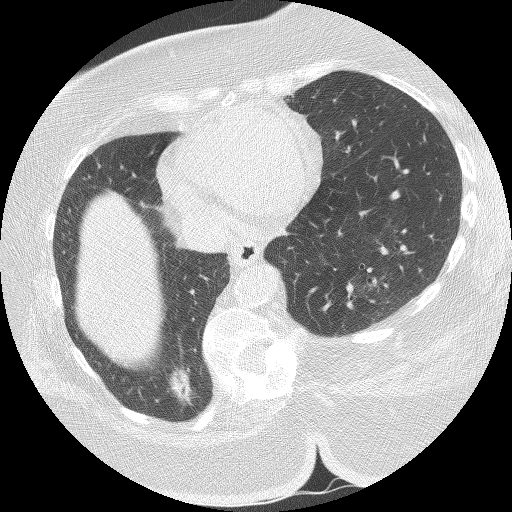
Chest CT (low-dose screening protocol), one axial image; first (baseline) screen; lung window (W 1500 / L -600 HU); 2.5 mm slice thickness; lung (sharp) reconstruction kernel (BONE); 512 × 512 image matrix, field of view 340 × 340 mm. Female participant, aged 59 years at enrolment. Former smoker at enrolment.
- Expert-annotated lung lesion, bounding box <144,347,204,417> (left, top, right, bottom; pixels).
- The exam's reader record, not a measurement of the box and not confirmed to be the same lesion: non-calcified nodule or mass ≥4 mm, right lower lobe, 21 × 10 mm, spiculated (stellate) margins, soft tissue attenuation.
- Official screen result: positive, change unspecified: nodule(s) >= 4 mm or enlarging nodule(s), mass(es), or other non-specific abnormalities suspicious for lung cancer.
- Later outcome: lung cancer diagnosed 52 days after this screen — bronchiolo-alveolar carcinoma, mucinous, right lower lobe, well differentiated (G1), stage IA (AJCC 6th edition), 15 mm at pathology.